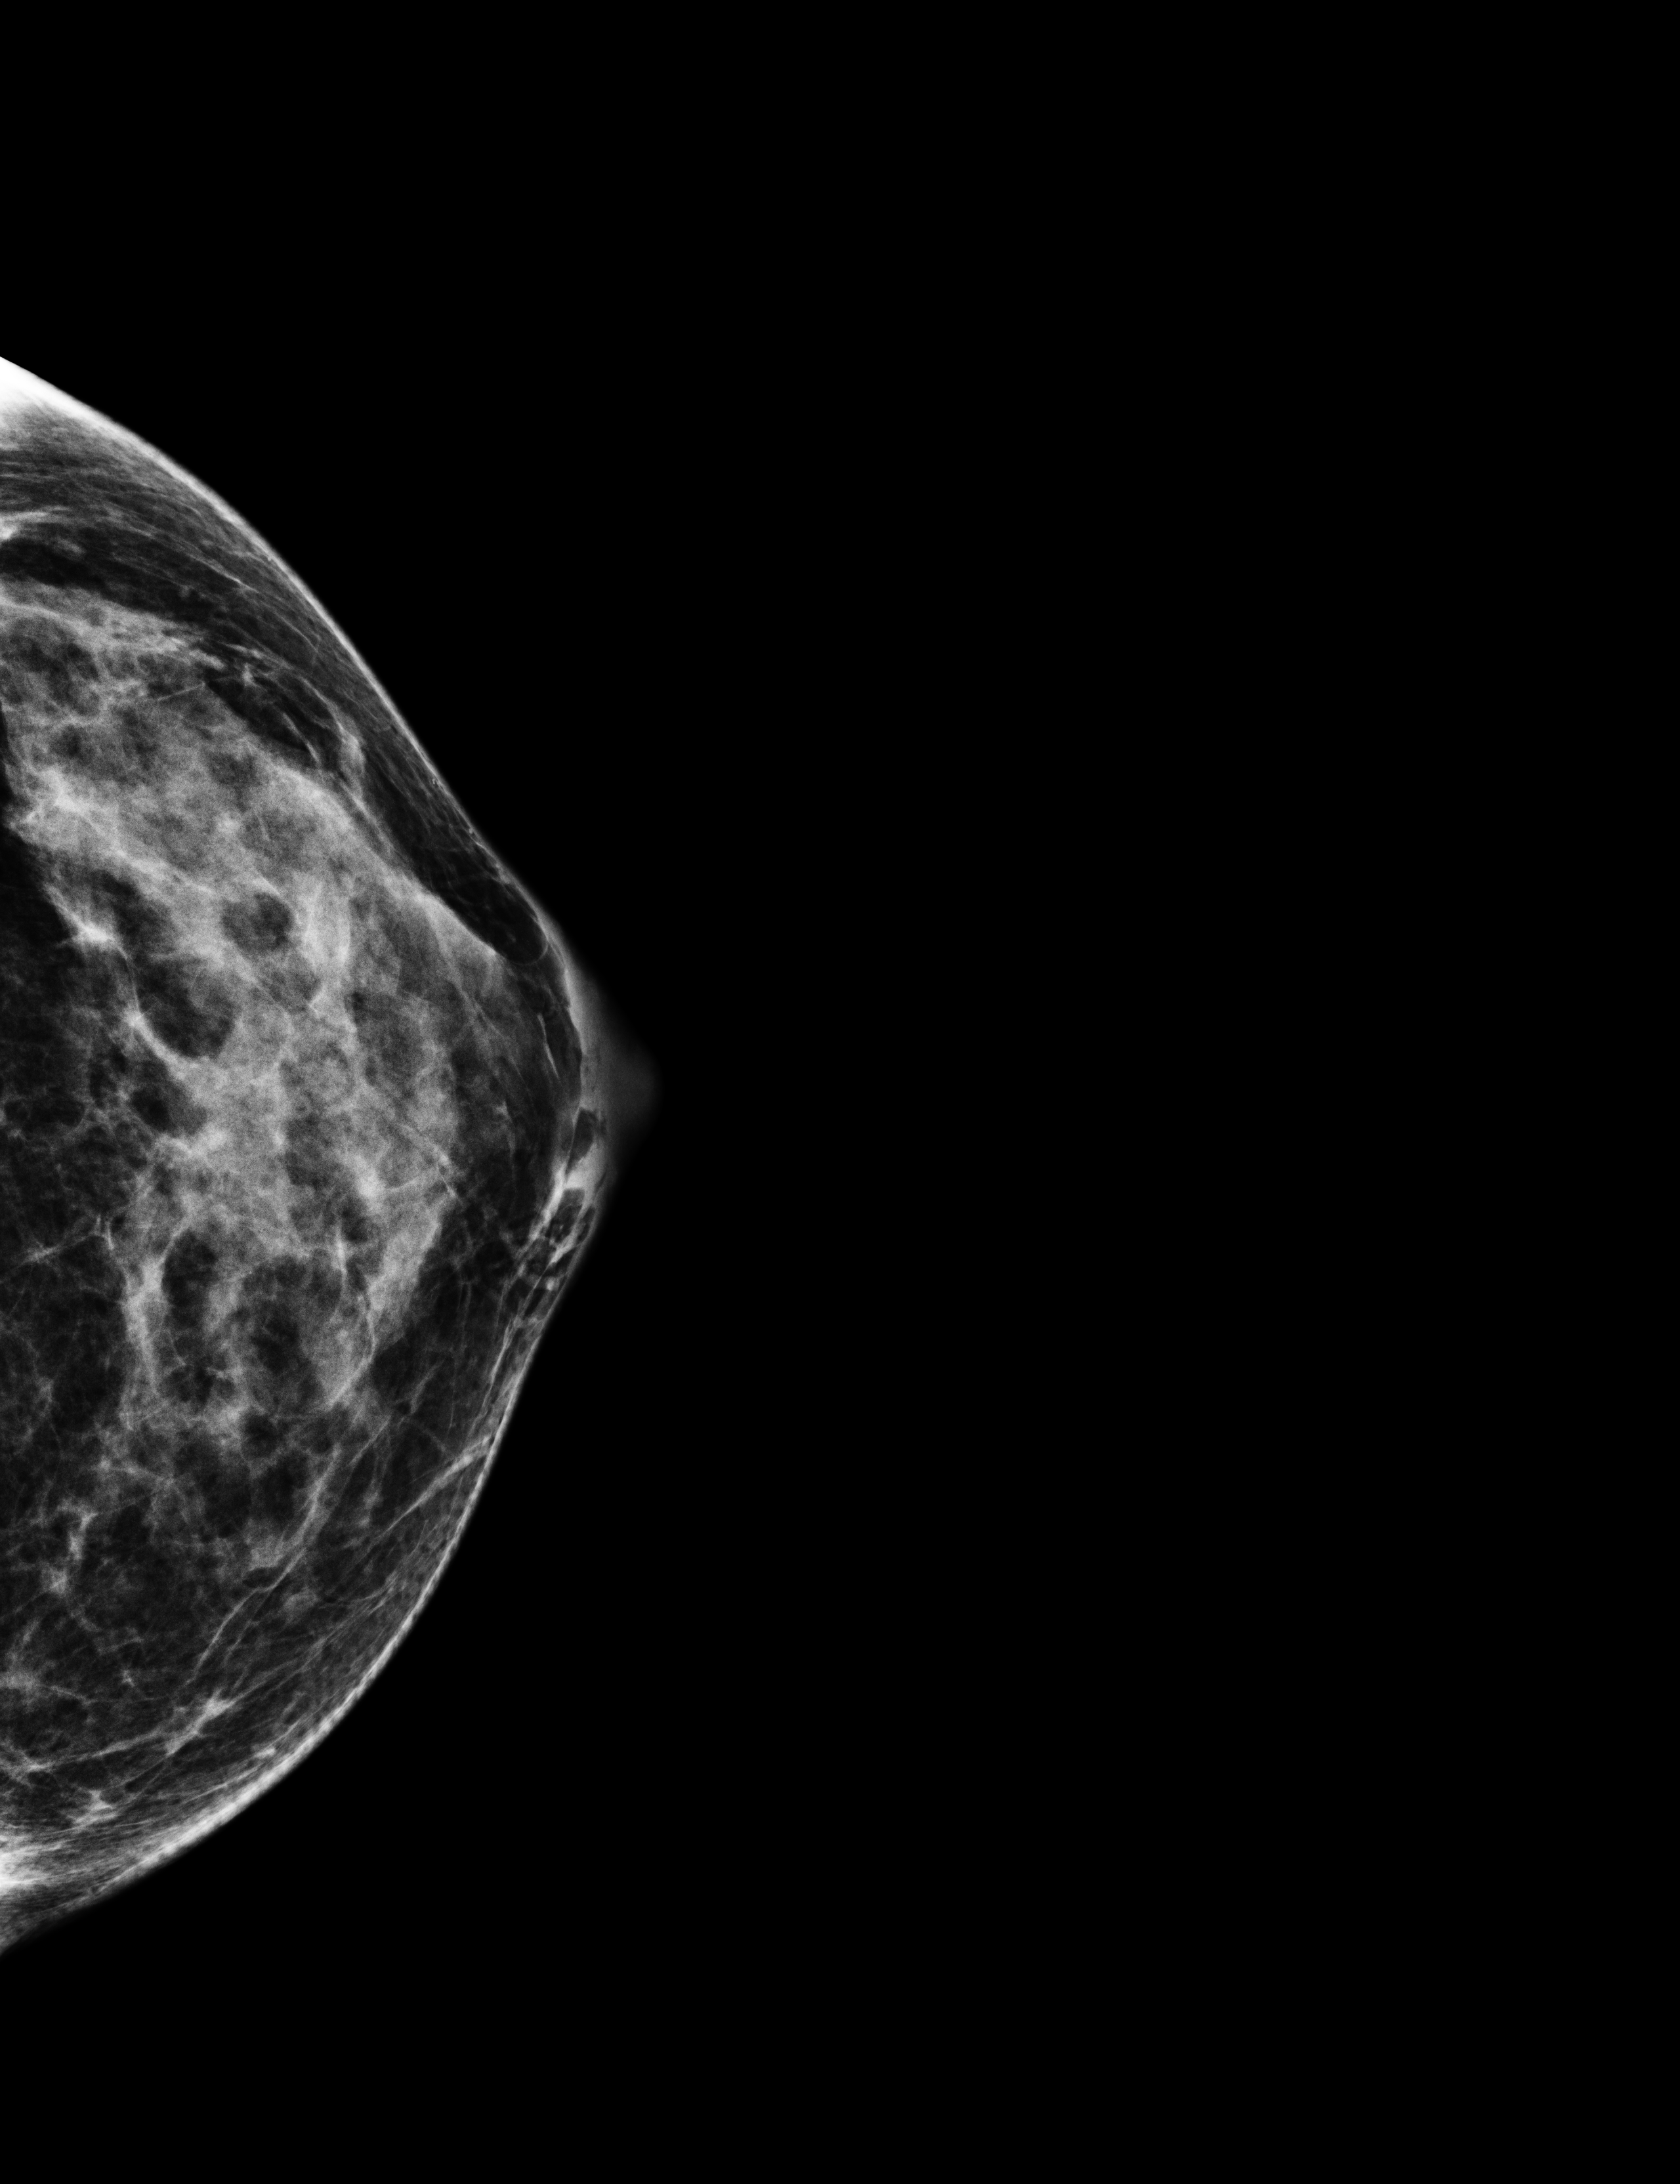
Full-field digital mammogram (FFDM); left breast; craniocaudal (CC) view; annual screening mammography examination. Female patient, age 51 years.
- breast density at the screening exam (both breasts): heterogeneously dense (BI-RADS density category c)
- final BI-RADS category for the screening round (tomosynthesis exam, both breasts): category 1
- recall: no recall after this screen